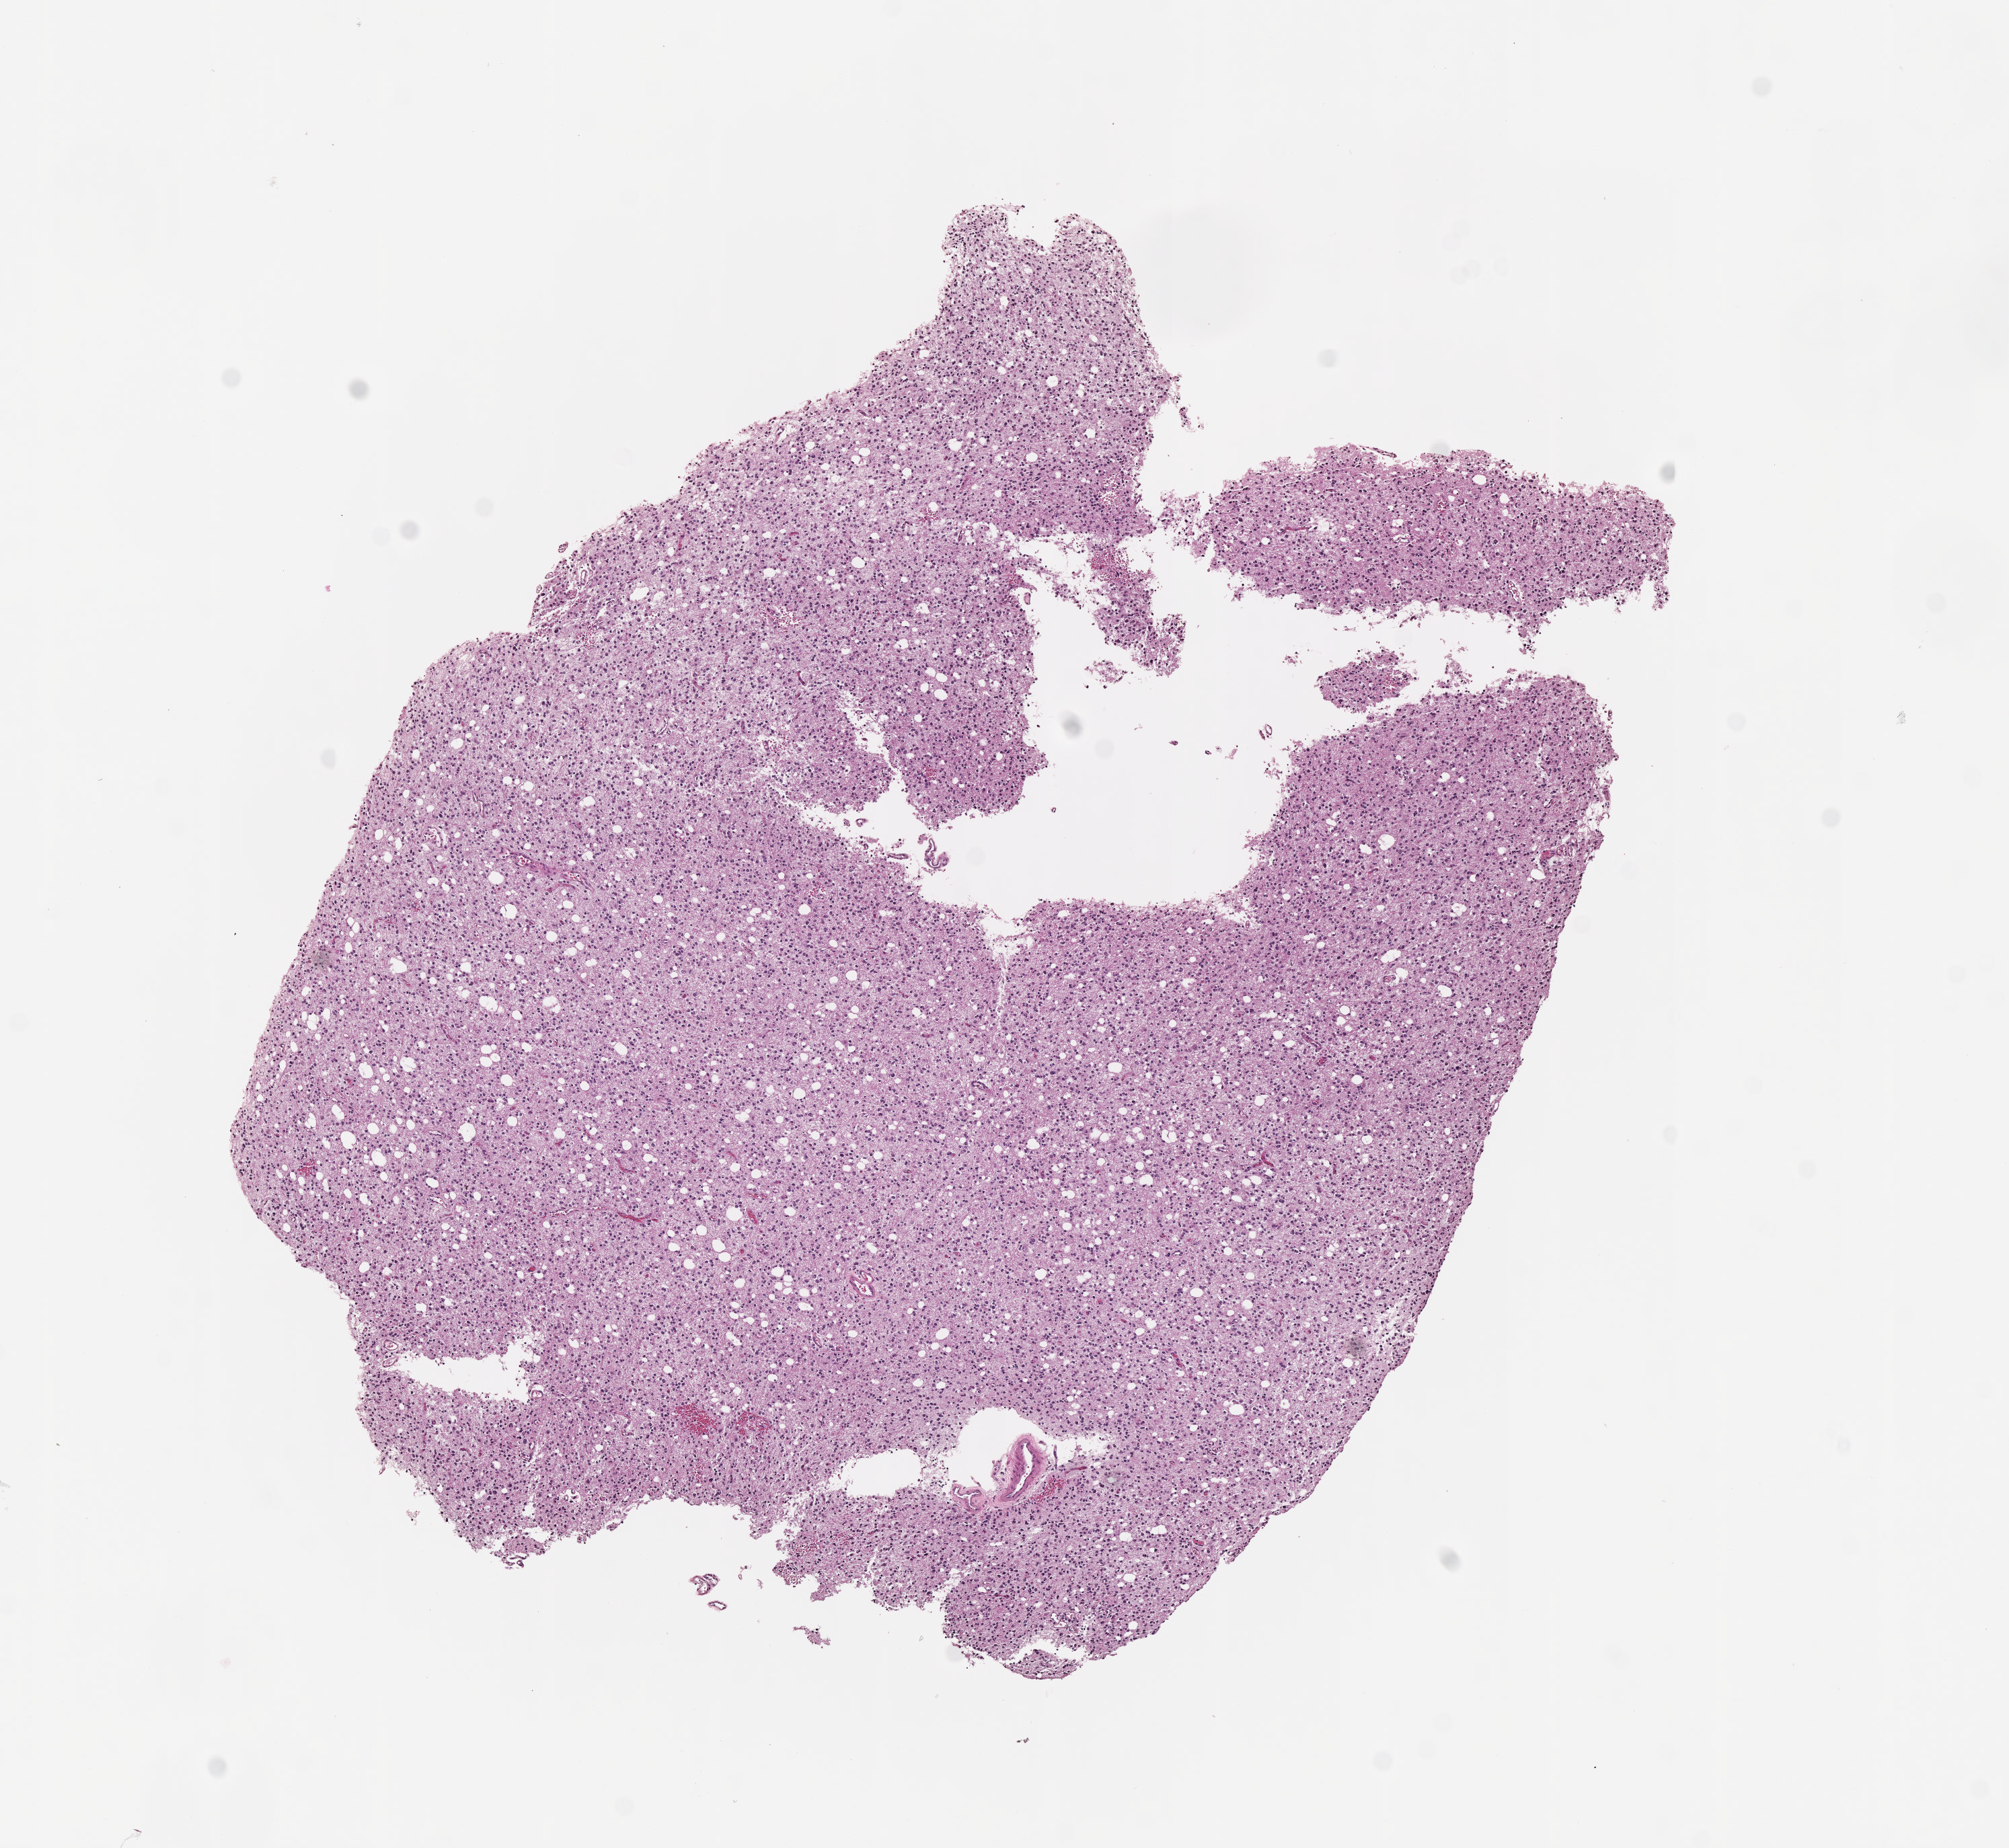
Digitized H&E tissue section (whole slide) — a low-resolution overview of the entire scanned area, about 6.0 x 5.6 mm (acquisition: 40x scan). FFPE section. Sample: primary tumour, brain. Patient: male, age at initial diagnosis 42 years.
Pathologic diagnosis: Oligodendroglioma, NOS (cerebrum).